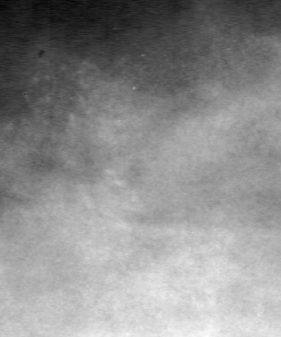
Cropped region of a digitized screen-film mammogram centred on a radiologist-marked abnormality, left breast, CC view.
Marked abnormality: calcifications, morphology pleomorphic, distribution clustered; BI-RADS assessment category 4; subtlety rating 2 on a 1 (subtle) to 5 (obvious) scale; pathology (as recorded): malignant.